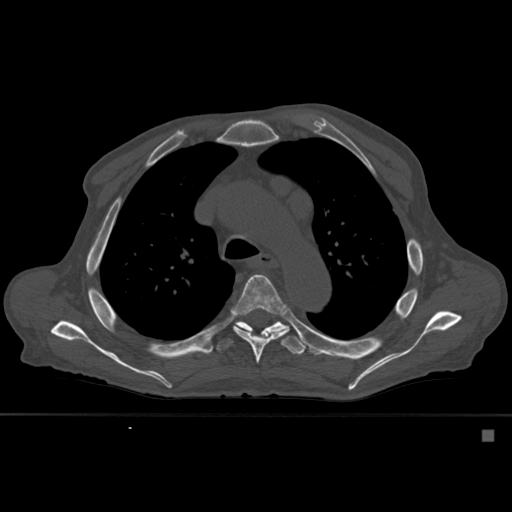
CT including the spine, one axial slice. Slice 397 of 527 in the series (ordered by position). Bone window (W 1800 / L 400 HU). 1.5 mm slice thickness. 512 × 512 image matrix. Male patient, age 78 years. Case-level facts recorded for this patient, not image findings: primary cancer: prostate.
Annotated regions visible in this slice (semi-automatically segmented with operator editing):
- T5 vertebra: bounding box <234,274,288,364> (left, top, right, bottom; pixels)
- T6 vertebra: <216,321,306,355>